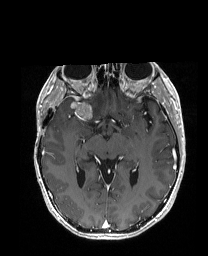
Brain MRI from a brain-tumour surgery series, one axial slice. Slice 103 of 192 in the series (ordered by position). T1-weighted post-contrast. 1 mm slice thickness. 208 × 256 image matrix, field of view 203 × 250 mm. Case-level facts recorded for this patient, not image findings: histopathology: Metastatic Carcinoma from Breast primary; tumour location: Right Frontal.
Structures marked on this image (expert manual segmentation):
- tumour: bounding box (x1, y1, x2, y2) in pixels: (55, 98, 104, 119)